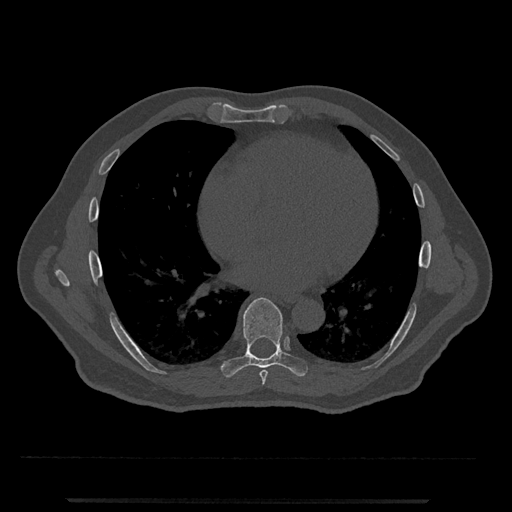
CT including the spine, one axial slice; slice 636 of 797 in the series (ordered by position); reconstruction kernel Br40s/3; bone window (W 1800 / L 400 HU); 0.5 mm slice thickness; 512 × 512 image matrix, field of view 419 × 419 mm. Male patient, age 63 years. Case-level facts recorded for this patient, not image findings: primary cancer: prostate.
Annotated regions visible in this slice (semi-automatic segmentation, software-assisted and operator-edited):
- T7 vertebra: bounding box [x1, y1, x2, y2] px = [259, 370, 268, 385]
- T8 vertebra: [221, 297, 308, 377]